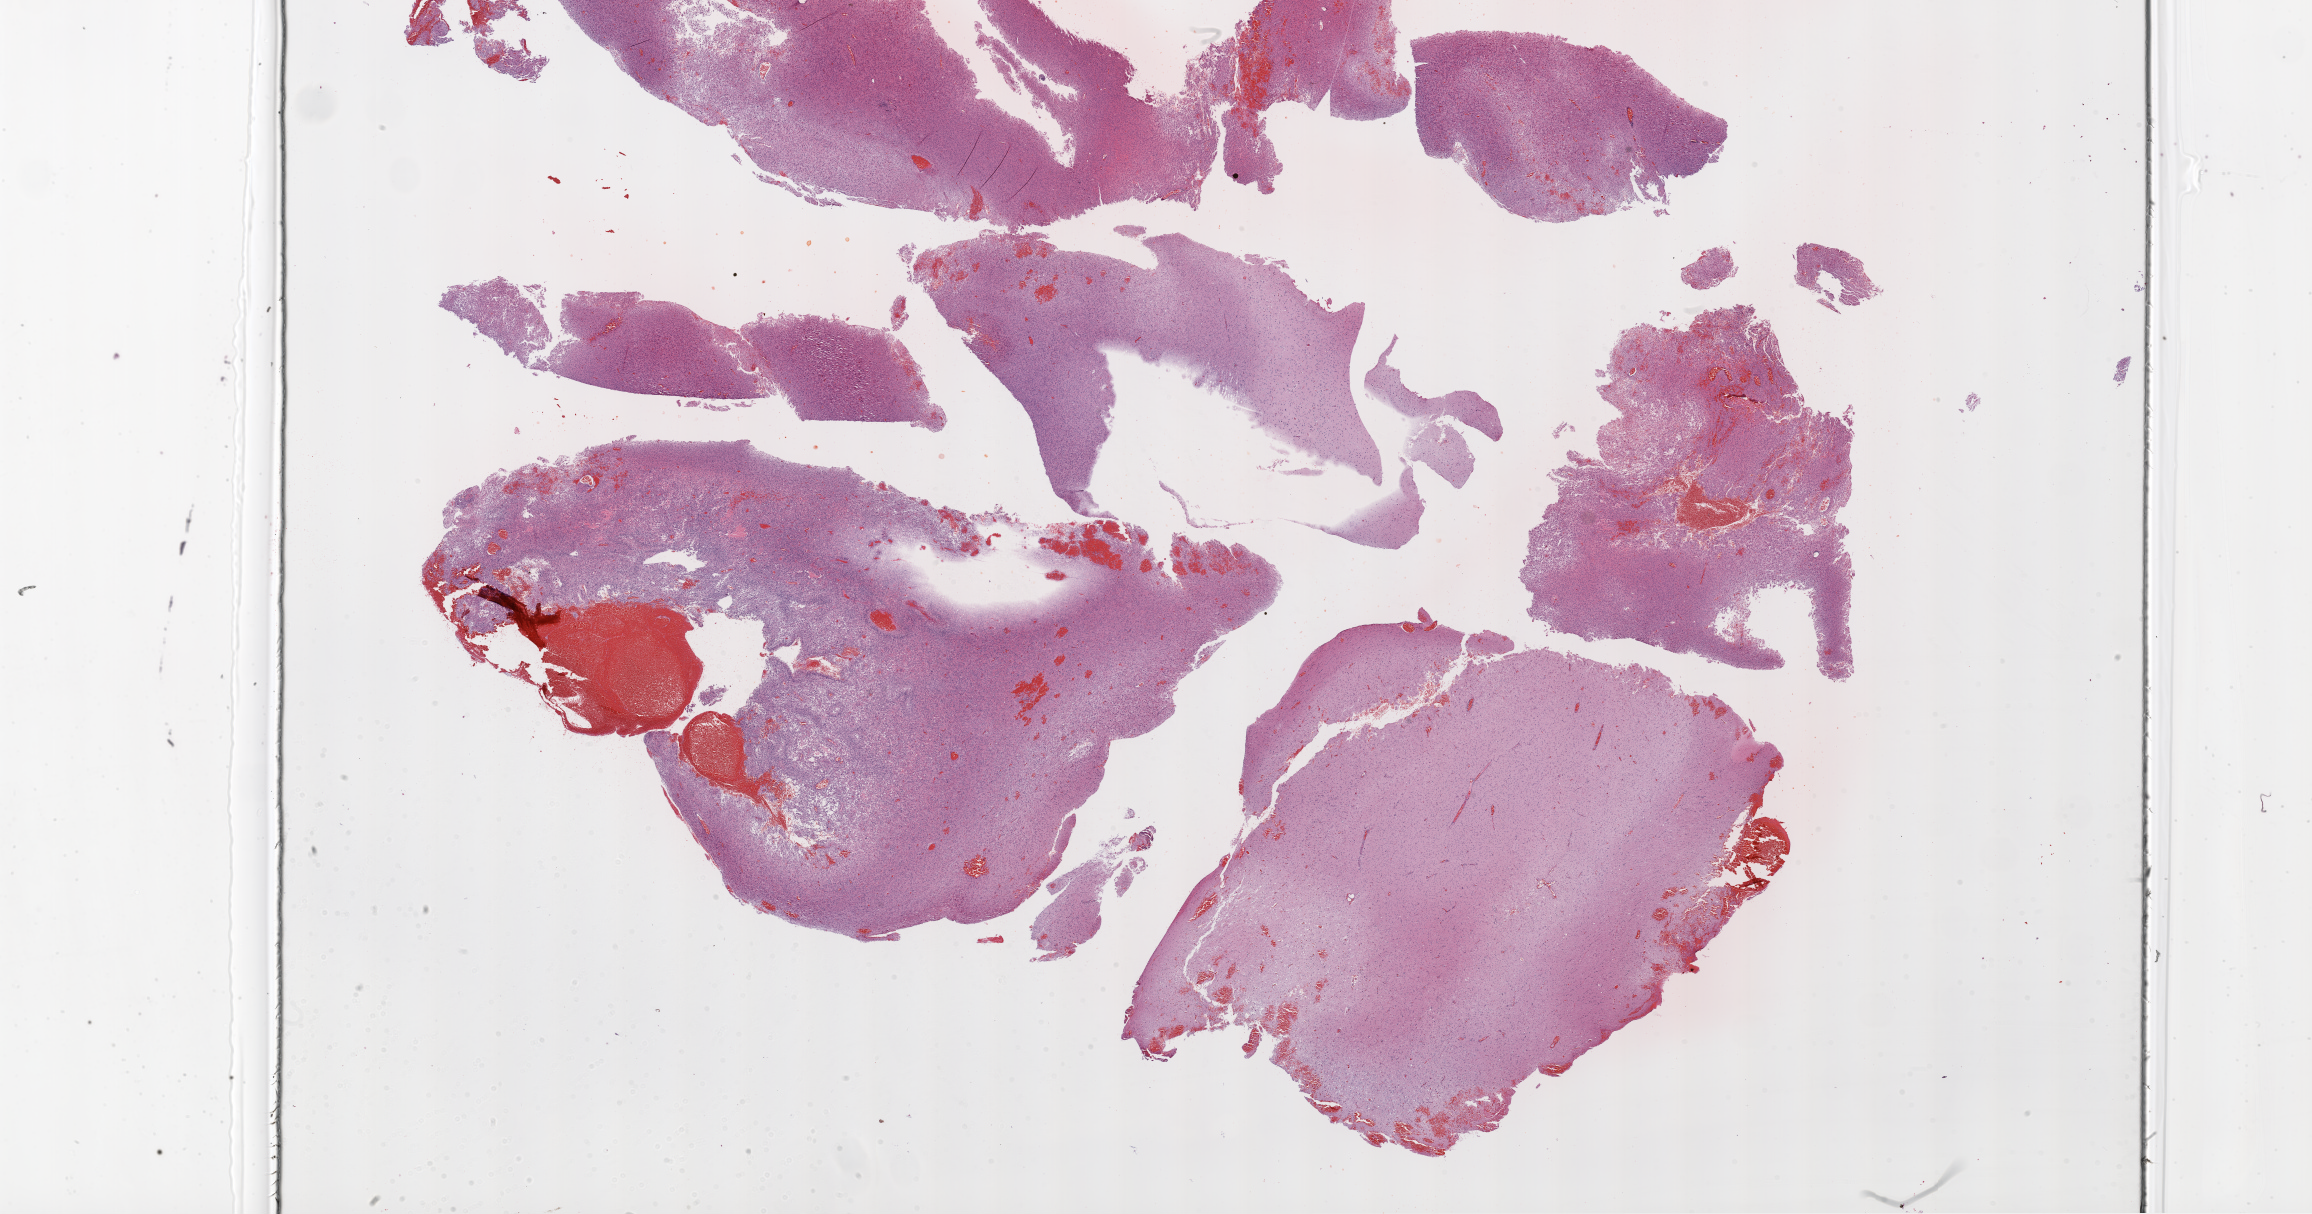
H&E whole-slide image, whole scanned area (about 37.1 x 19.5 mm) shown as a low-resolution overview. Formalin-fixed paraffin-embedded (FFPE) diagnostic section. Brain, primary tumour sample. Patient: male, age at initial diagnosis 60 years.
Pathologic diagnosis: Glioblastoma.